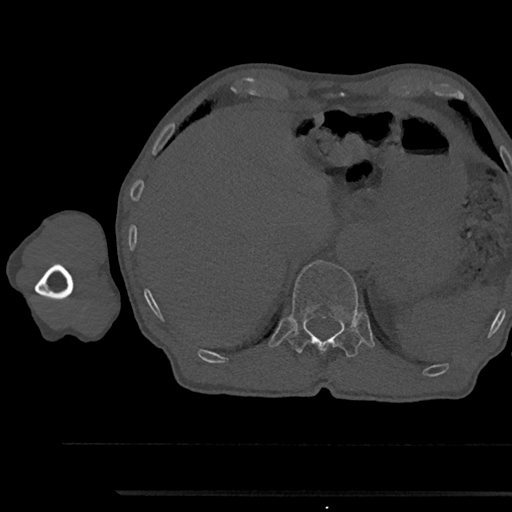
CT including the spine, one axial slice. Position 721 of 797 along the scan axis. Reconstruction kernel Br40s/3. 120 kVp. Bone window (W 1800 / L 400 HU). 0.5 mm slice thickness. 512 × 512 image matrix, field of view 367 × 367 mm. Patient: male, 79 years. Case-level facts recorded for this patient, not image findings: primary cancer: prostate.
Outlined on this slice (semi-automatically segmented with operator editing):
- T12 vertebra: bounding box (x1, y1, x2, y2) in pixels: (289, 260, 362, 357)